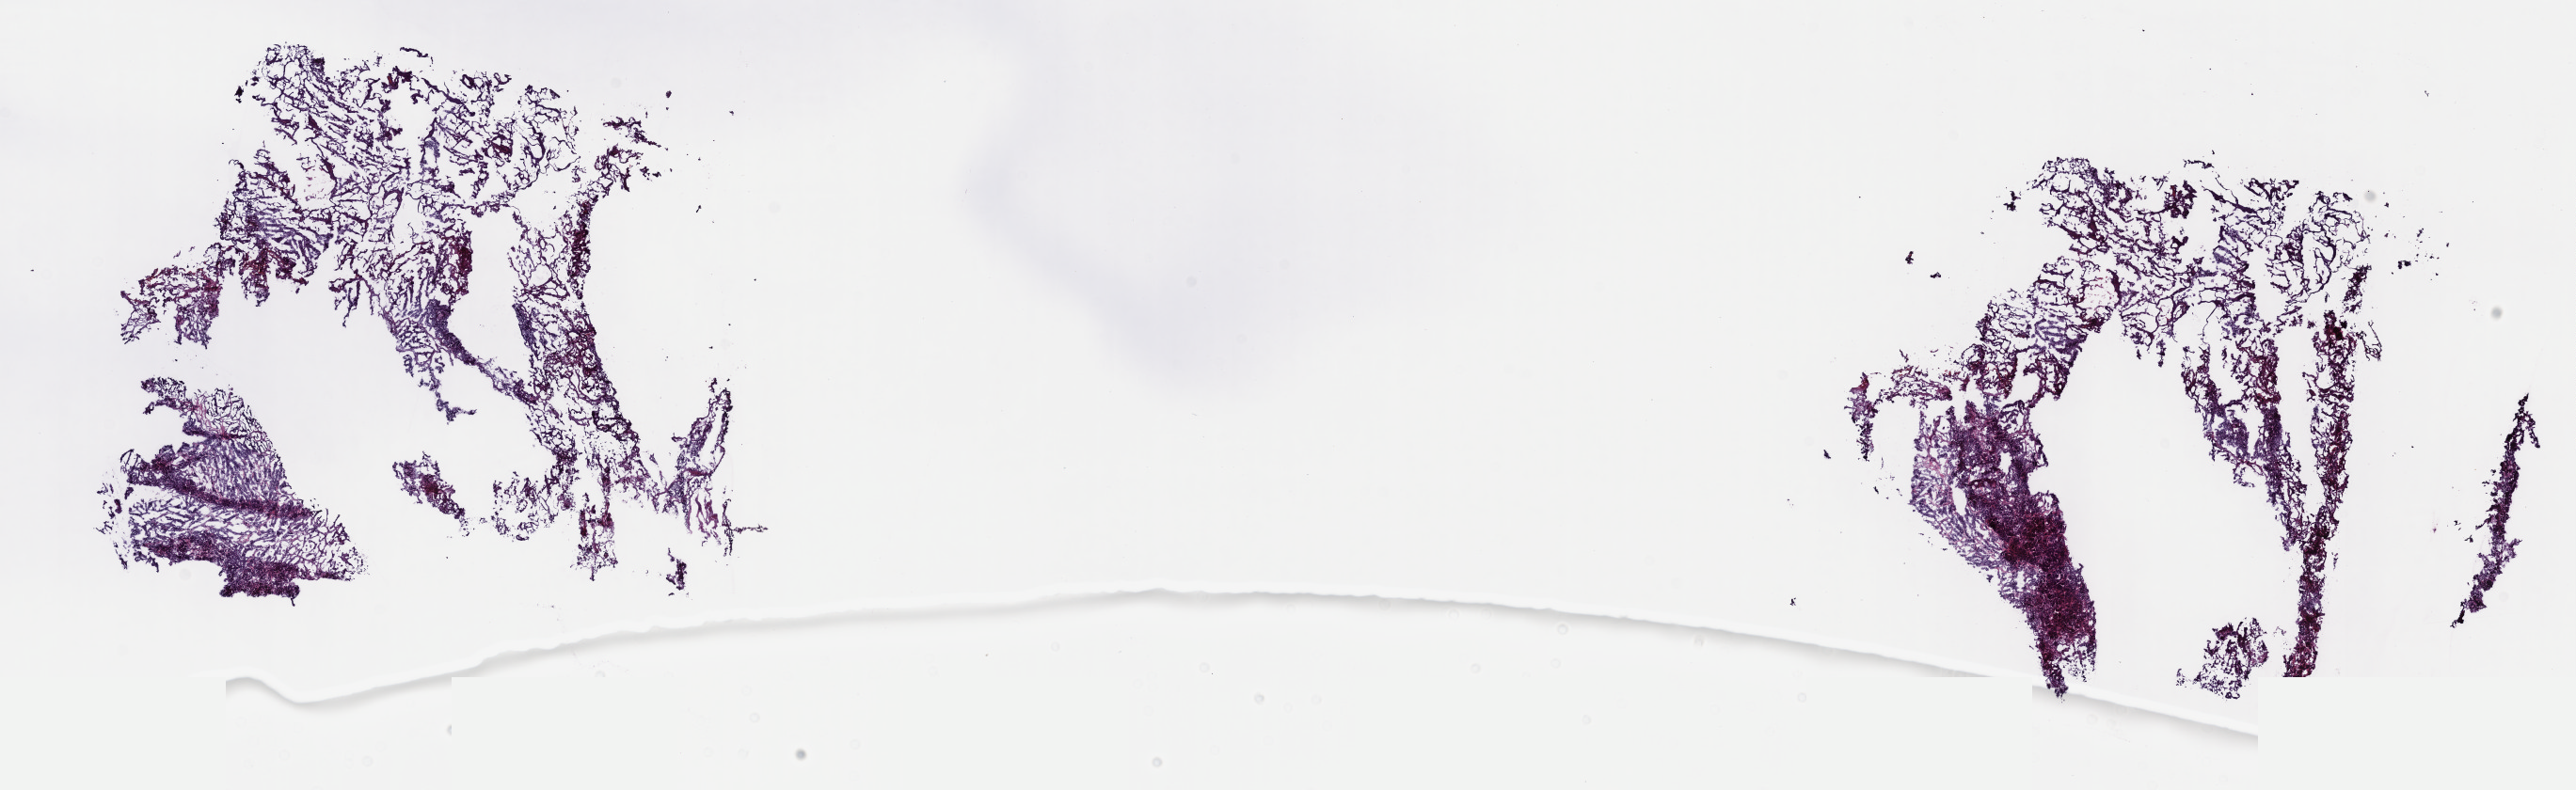
Whole-slide histology image, H&E-stained — low-resolution overview of the scanned area, about 22.1 x 6.8 mm (acquisition: 40x scan); frozen section from the top of the tissue portion; sample: primary tumour, bladder. Patient: male, age at initial diagnosis 77 years.
Diagnosis: Transitional cell carcinoma.